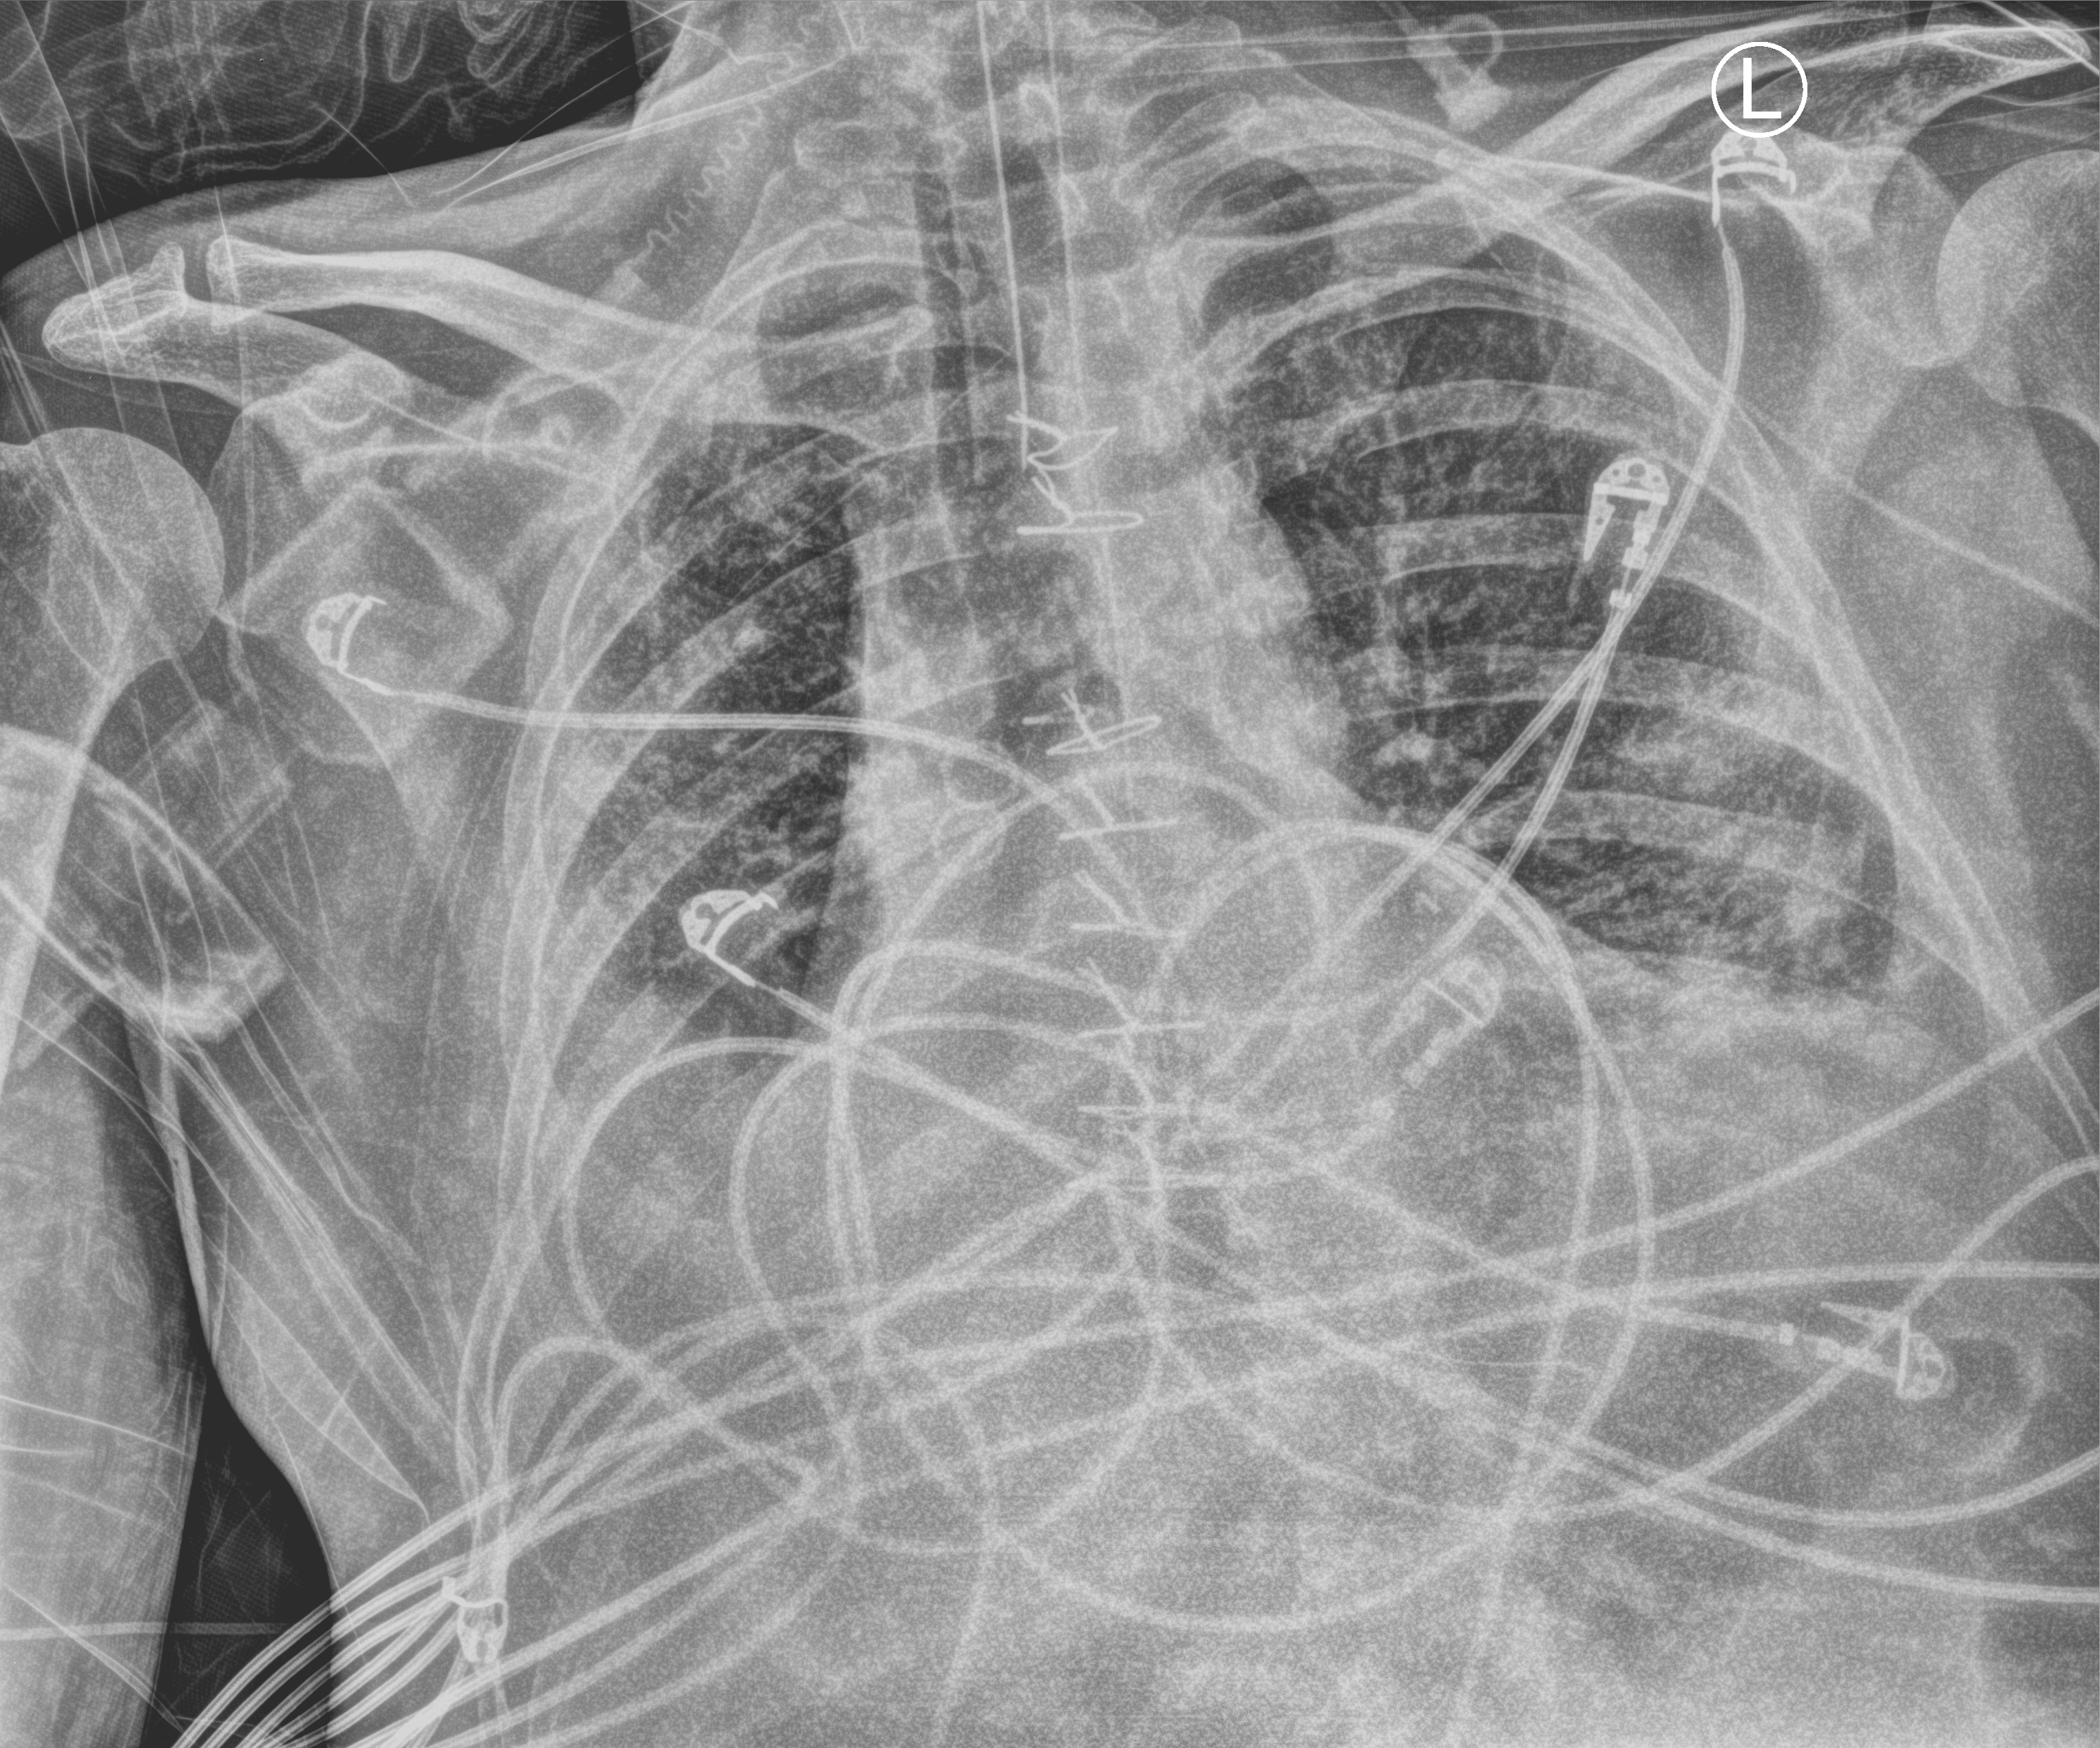
Bedside chest radiograph (computed radiography). Patient hospitalised with COVID-19; male, aged 18–59 years.
Admission-level facts for this patient (not findings on this image; timing relative to this image not recorded): mechanically ventilated during this hospital stay: yes.